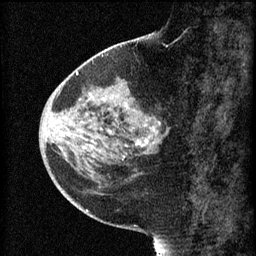
Breast MRI (dynamic contrast-enhanced), one sagittal slice; position 26 of 60 along the scan axis; 3 images stored at this slice position (order not interpretable as contrast timing); 1.5 T; TE 4.2 ms, TR 8.2 ms; 2 mm slice thickness; 256 × 256 image matrix. Patient: female, 44 years.
Annotated regions visible in this slice (semi-automatic segmentation, software-assisted and operator-edited):
- analysis volume of interest (the breast-tissue region the enhancement analysis was run in; not a lesion): bounding box <73,82,169,165> (left, top, right, bottom; pixels)
- tumour enhancement mask (voxels above the 70 % enhancement threshold inside the analysis volume of interest): <88,92,162,159>